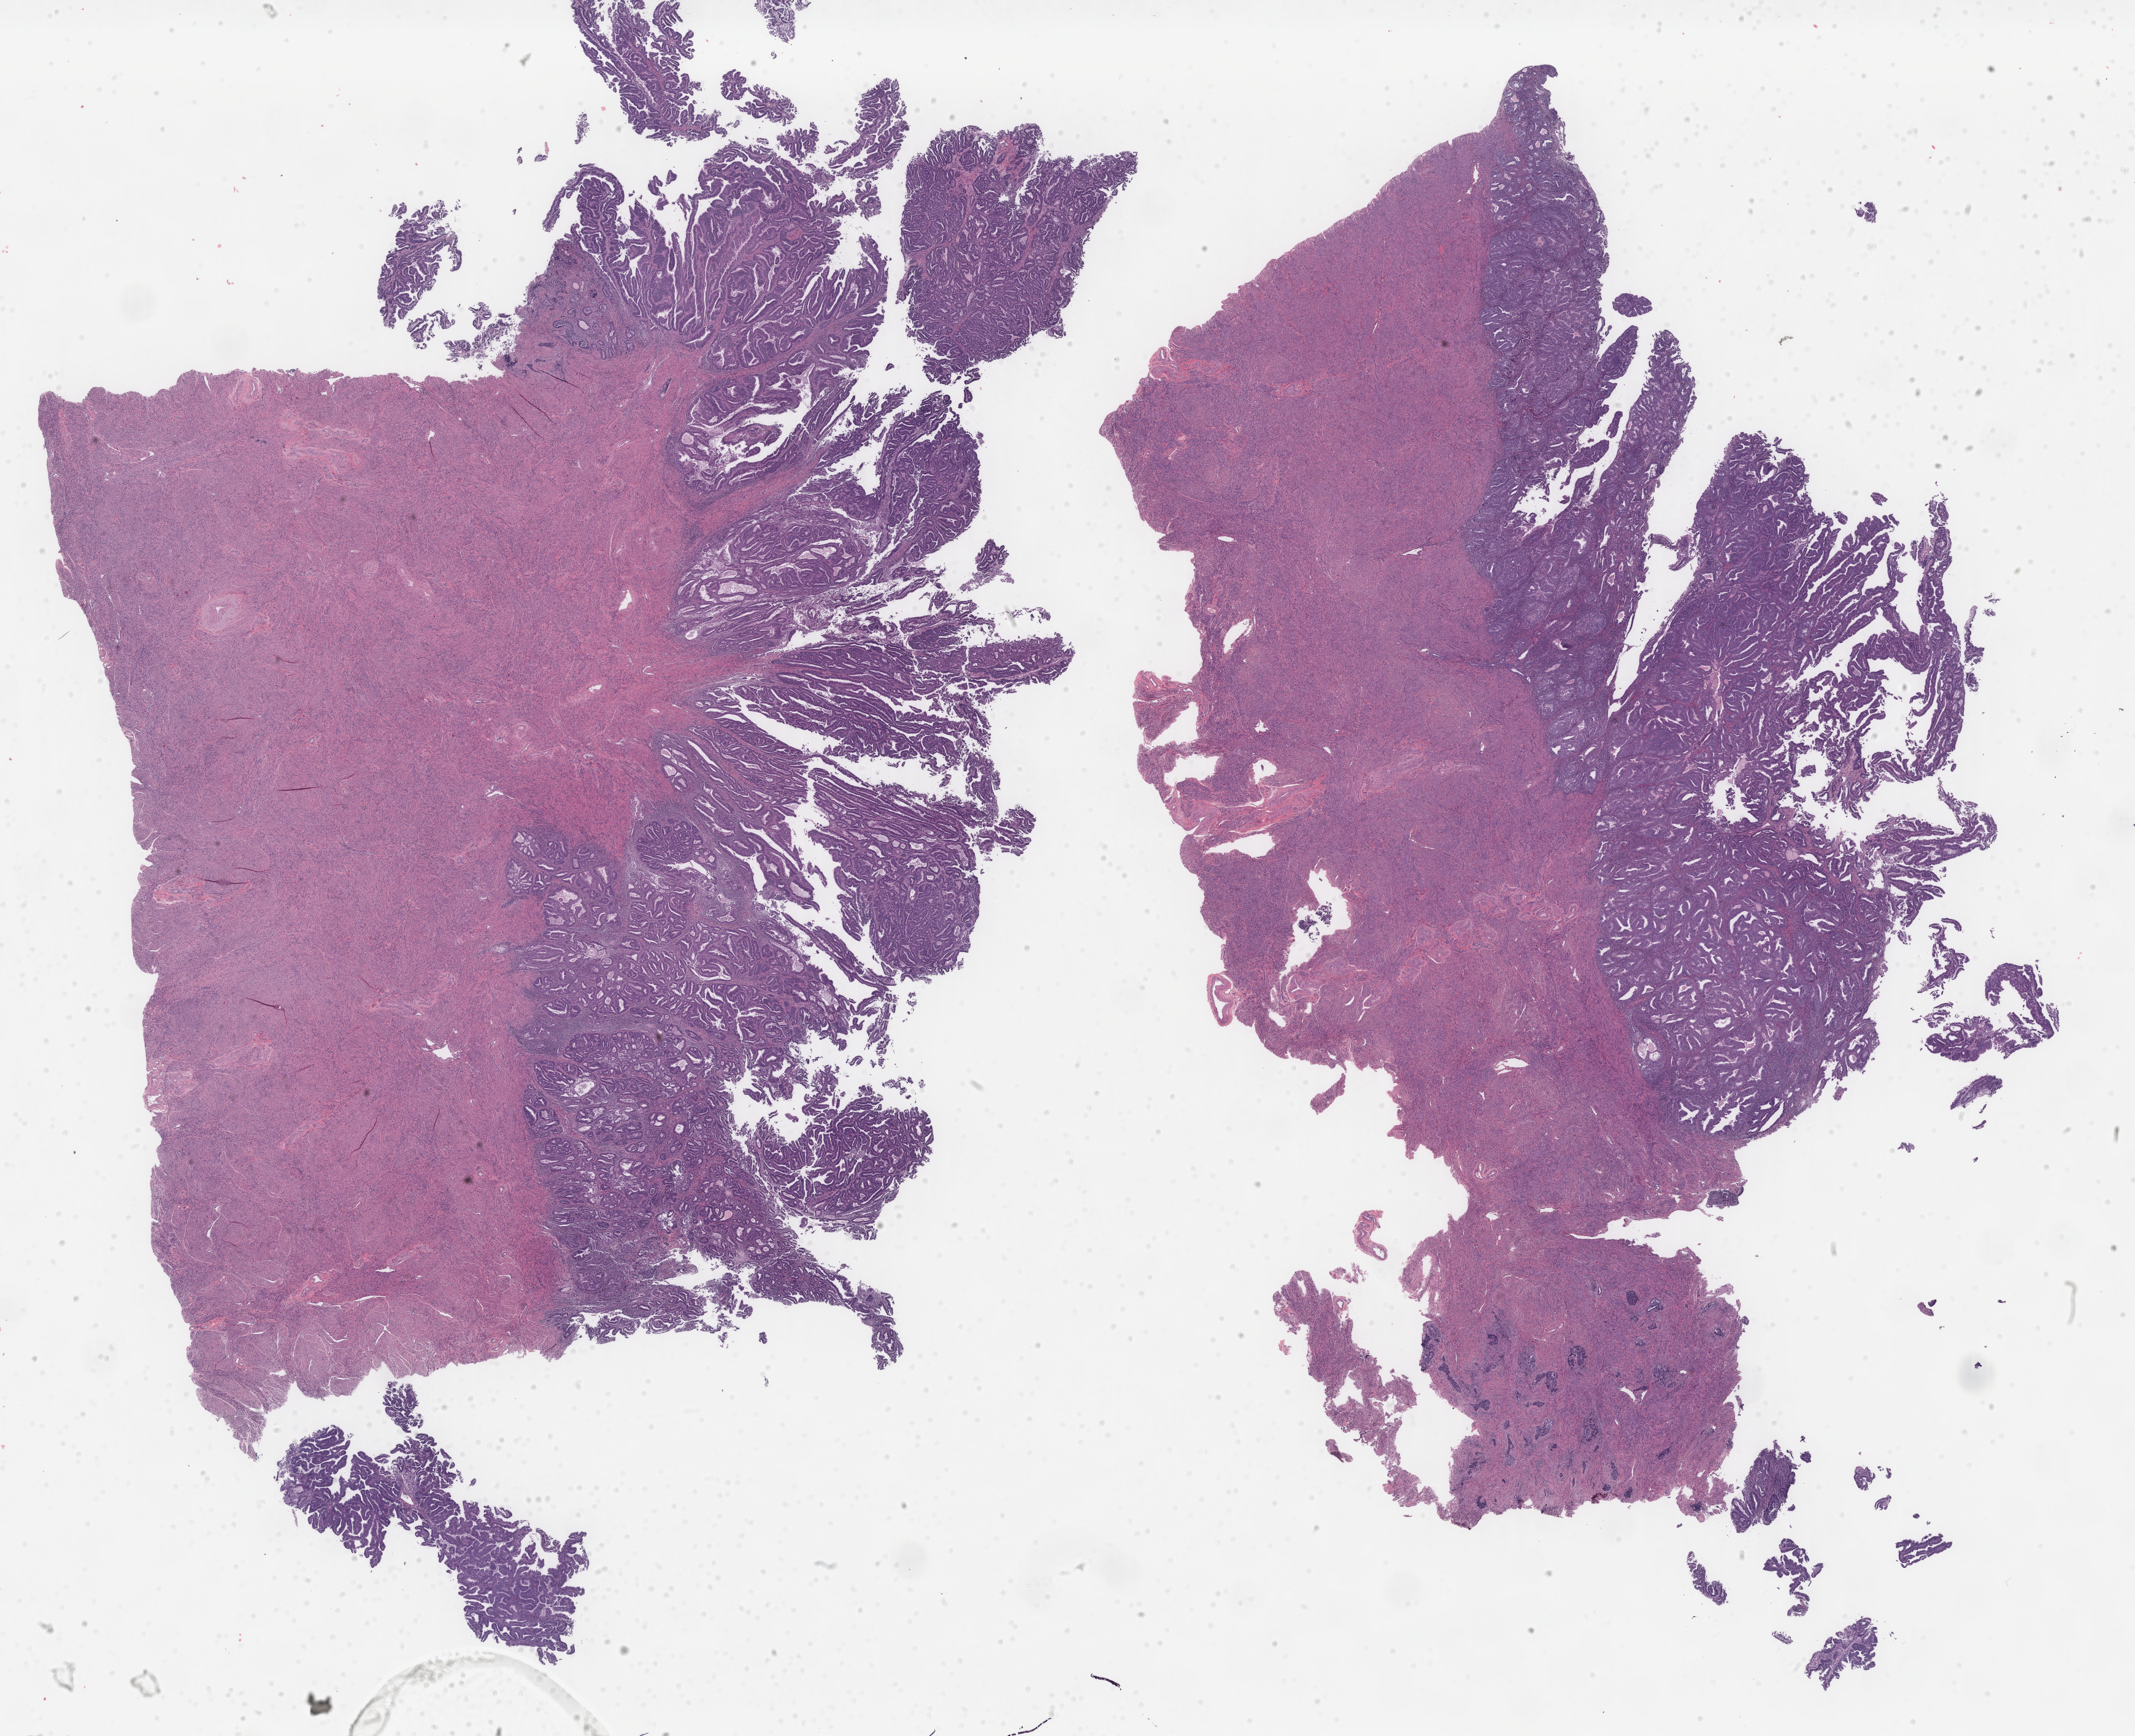
H&E-stained whole-slide image, low-resolution overview of the scanned area, about 27.6 x 22.5 mm (slide scanned at 40x); FFPE section; uterus, primary tumour sample. Patient: female, age at initial diagnosis 60 years. Histologic grade: G1 (well differentiated).
• pathologic diagnosis: Endometrioid adenocarcinoma, NOS
• FIGO stage: IA